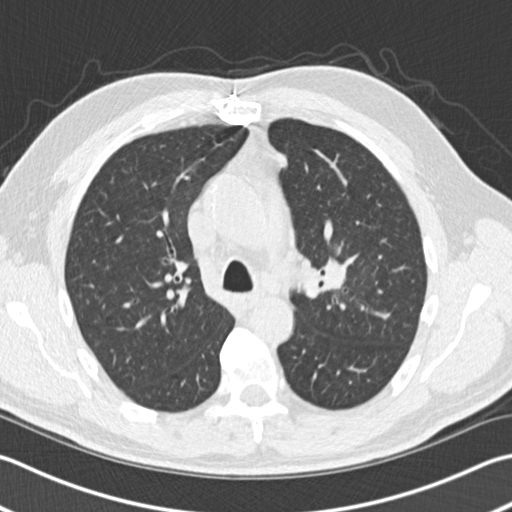
Low-dose screening chest CT, one axial slice. Position 103 of 153 along the scan axis. 120 kVp. Lung window (W 1500 / L -600 HU). 2 mm slice thickness. 512 × 512 image matrix, field of view 346 × 346 mm.
Outlined on this slice (manually delineated by an expert):
- lesion 1 (tumor, upper lobe of left lung): bounding box [x1, y1, x2, y2] px = [326, 263, 346, 289]